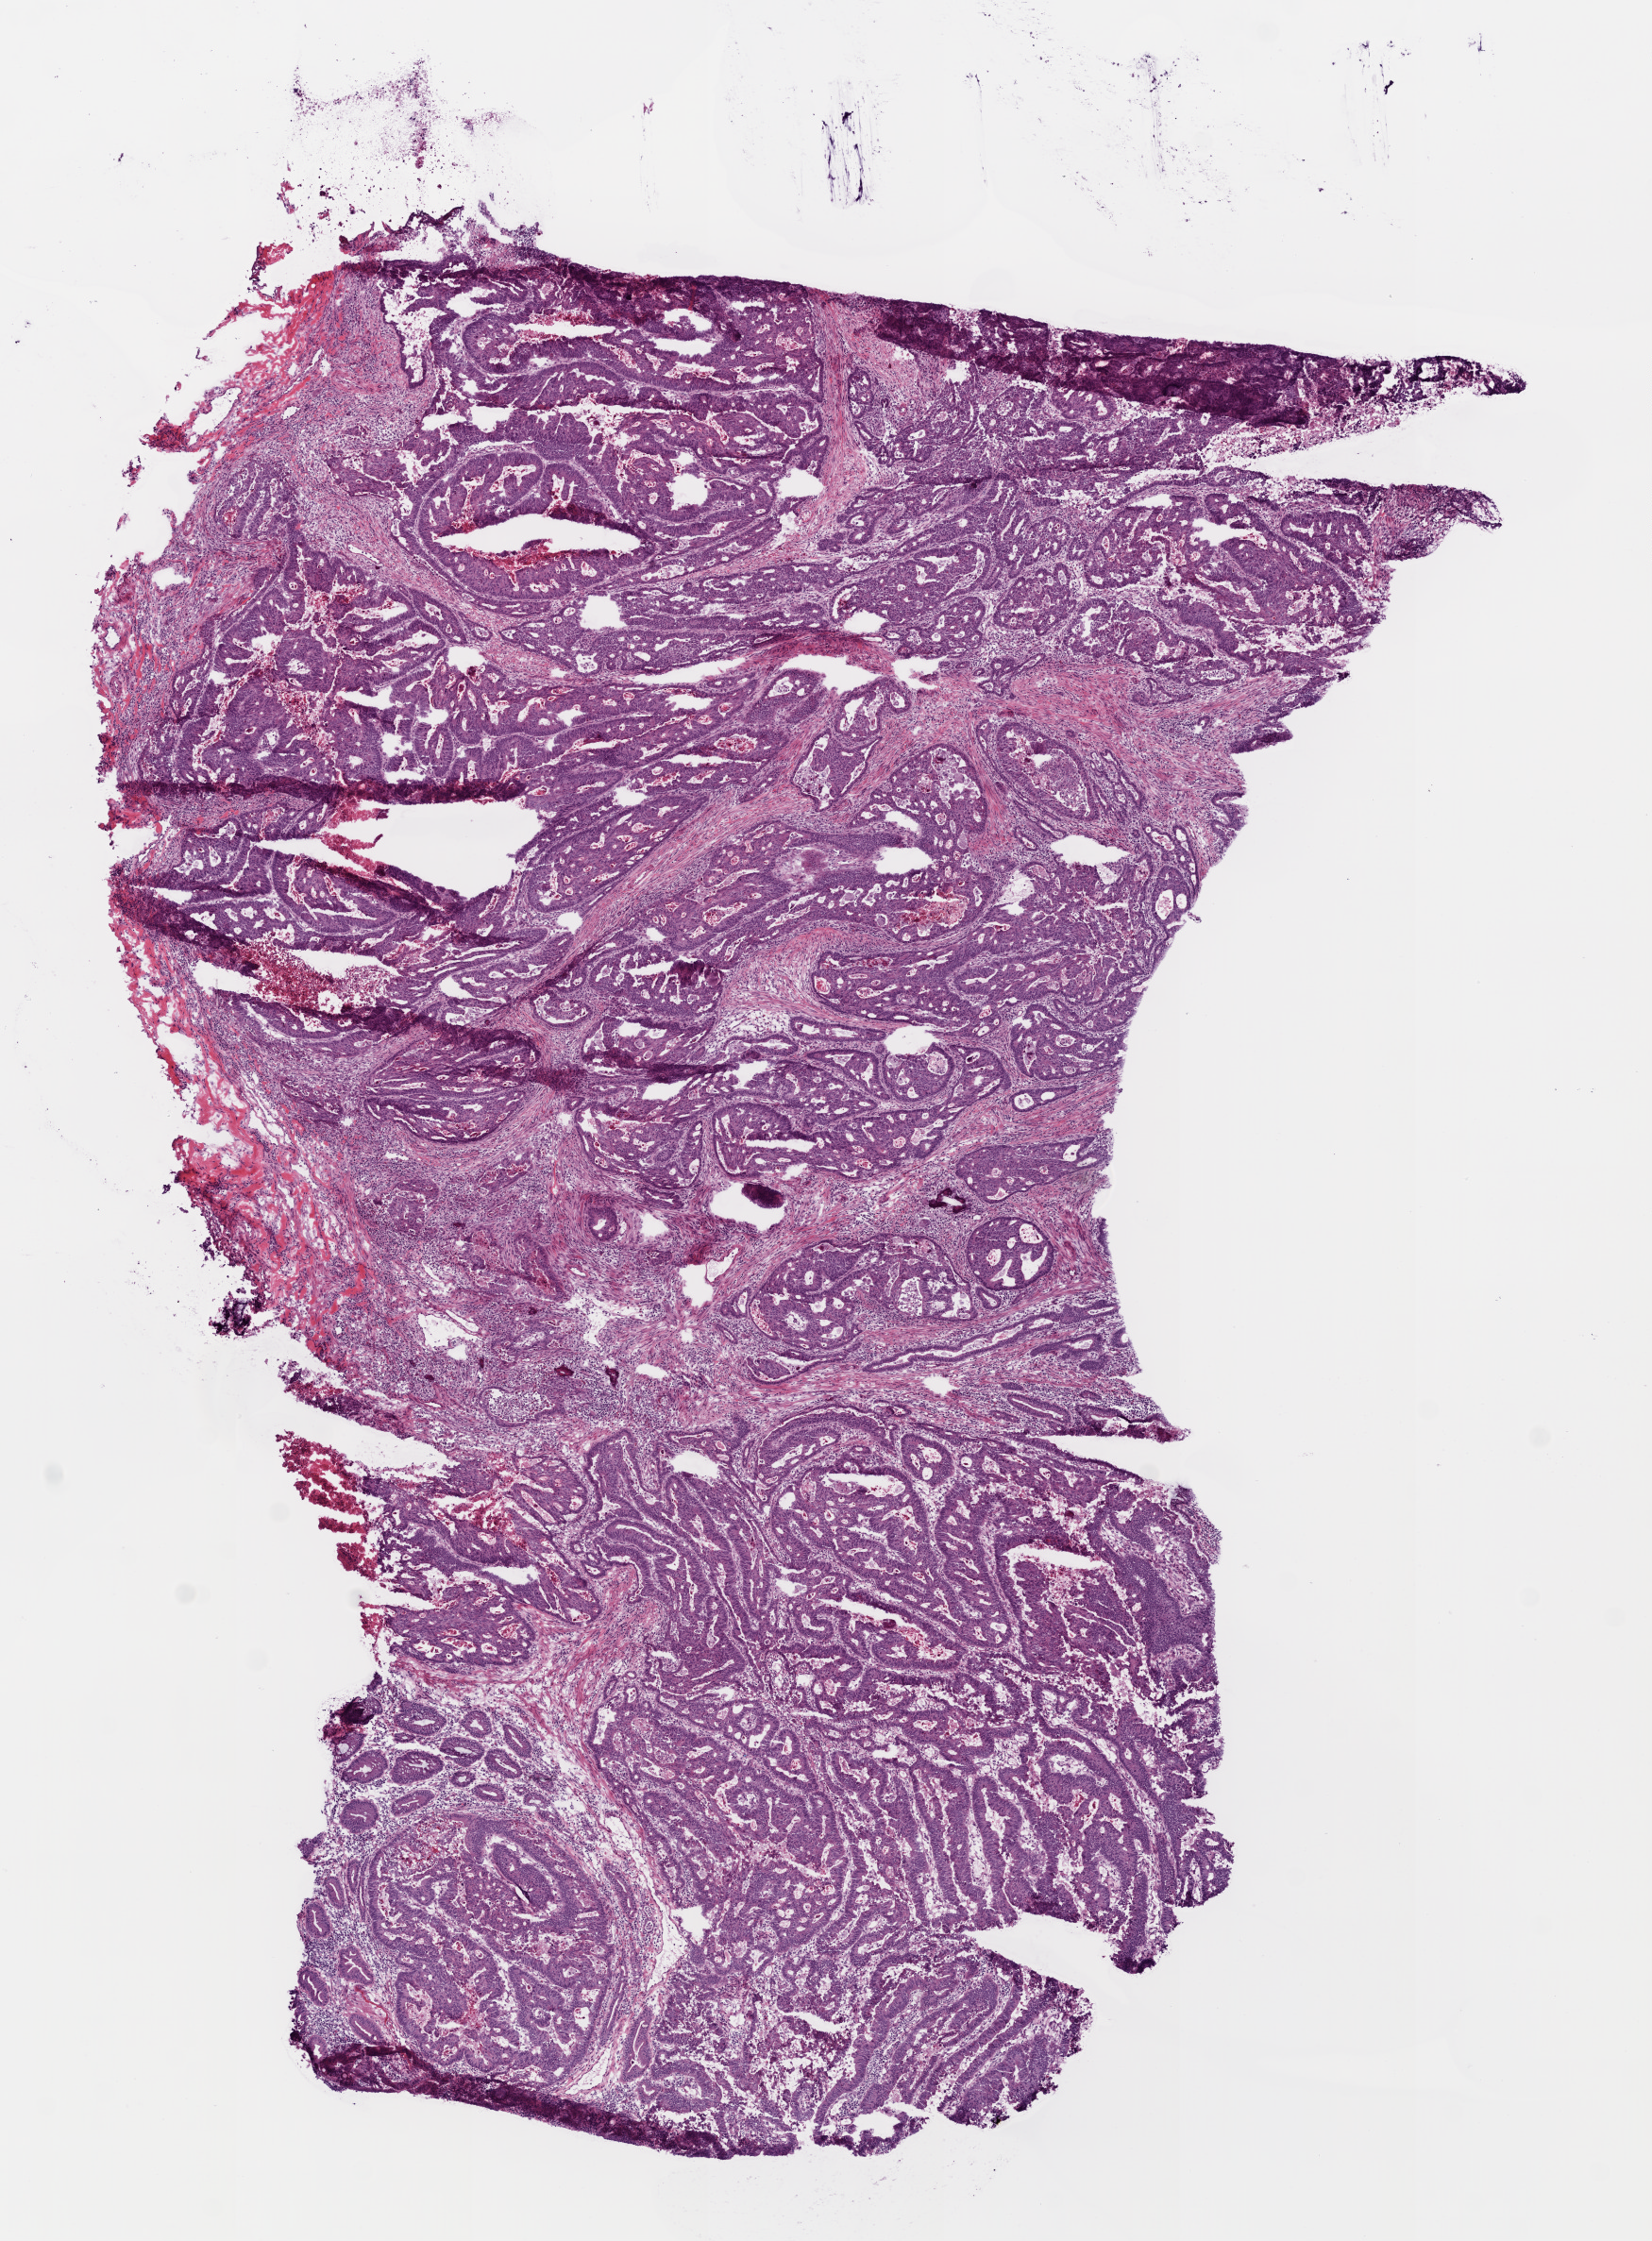
H&E-stained whole-slide image, a low-resolution overview of the entire scanned area, about 7.0 x 9.5 mm (slide scanned at 20x); frozen section; primary tumour sample from the colon. Male patient; age at initial diagnosis 64 years. Slide review estimates, as recorded: tumour cells 90%, tumour nuclei 90%, normal cells 0%, stromal cells 10%, necrosis 0%.
Lymph nodes positive (case pathology): 0 of 27 examined. AJCC pathologic stage: IIA (6th edition). Pathologic diagnosis: Adenocarcinoma, NOS (descending colon).